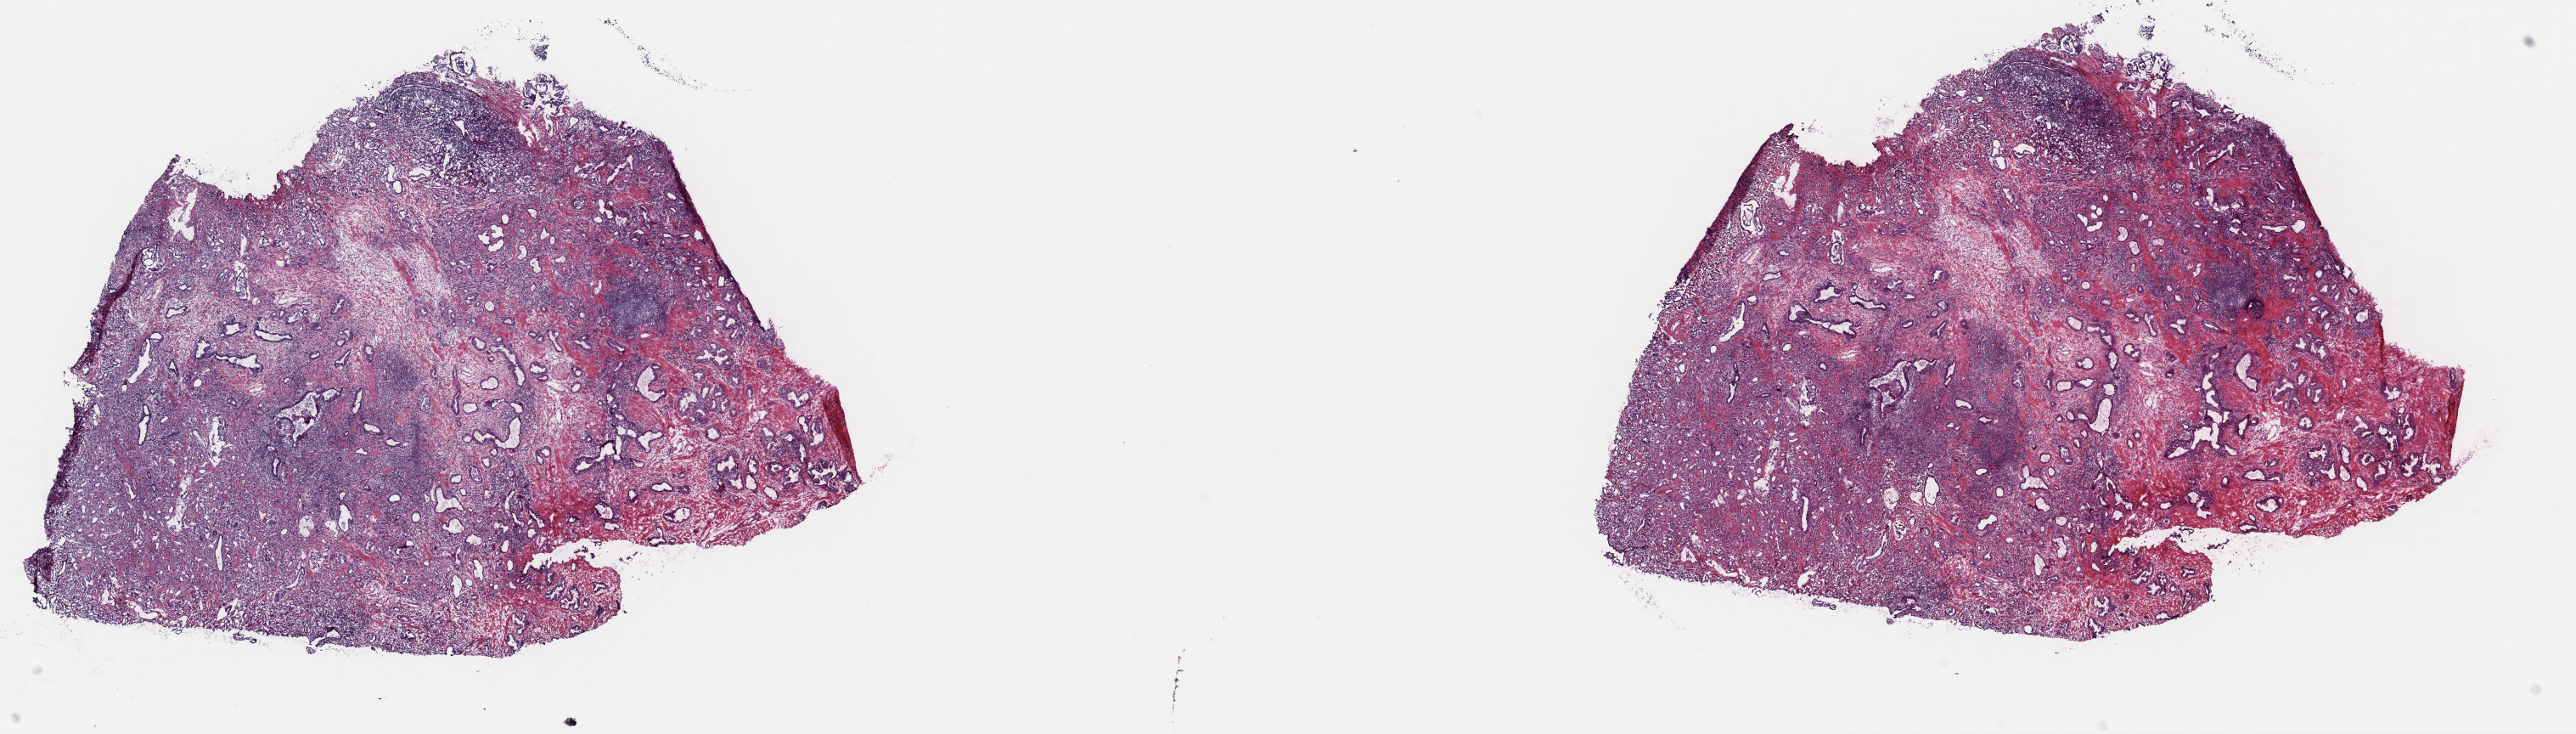
Whole-slide histology image, H&E-stained — a low-resolution overview of the entire scanned area, about 24.0 x 6.8 mm (from a 40x scan). Frozen section from the top of the tissue portion. Sample: primary tumour, prostate. Patient: male, age at initial diagnosis 68 years. Gleason score: 8 (4+4). Slide review estimates, as recorded: tumour cells 80%, tumour nuclei 80%, normal cells 5%, stromal cells 15%, necrosis 0%. Inflammatory infiltration, as recorded: lymphocyte infiltration 40%, monocyte infiltration 20%, neutrophil infiltration 20%.
• lymph nodes positive (case pathology): 0 of 2 examined
• laterality: bilateral
• pathologic diagnosis: Adenocarcinoma, NOS